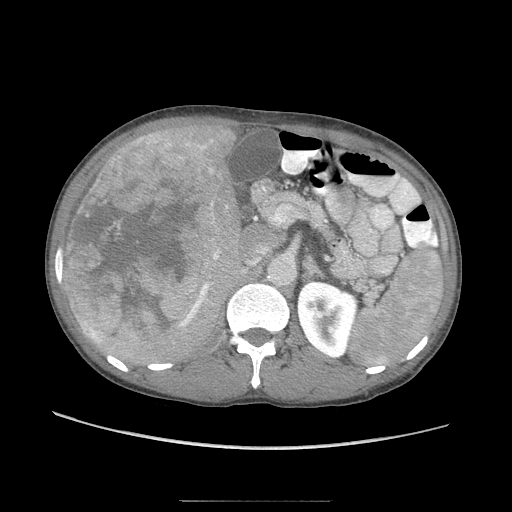
Contrast-enhanced abdominal CT (liver protocol), one axial slice; position 44 of 103 along the scan axis; reconstruction kernel STANDARD; 120 kVp; soft-tissue window (W 400 / L 40 HU); 2.5 mm slice thickness; 512 × 512 image matrix, field of view 380 × 380 mm. From the clinical record (not read from this slice): diagnosis: hepatocellular carcinoma (patient treated with transarterial chemoembolisation; whether this scan precedes or follows treatment is not stated here); TNM stage (as recorded): Stage-IIIA; Child-Pugh class: A; tumour differentiation: moderately differentiated; tumour nodularity: multinodular.
Outlined on this slice (semi-automatic segmentation, software-assisted and operator-edited):
- liver parenchyma outside the tumour (the mass and vessels are separate outlines, so this box may not span the whole liver): bounding box (x1, y1, x2, y2) in pixels: (62, 120, 252, 368)
- mass: (62, 130, 220, 347)
- liver vessels: (197, 153, 222, 298)